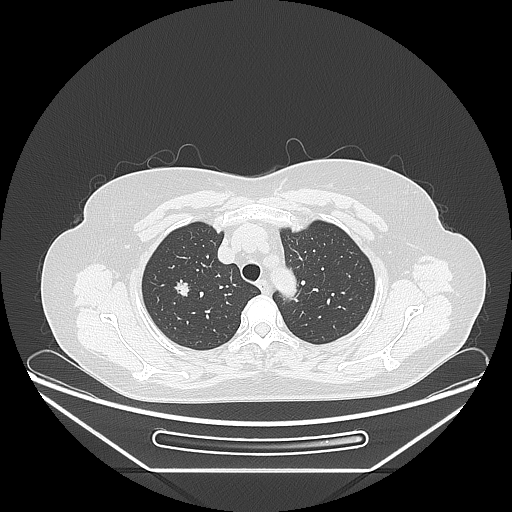
Chest CT, one axial slice; slice 197 of 236 in the series (ordered by position); 120 kVp; lung window (W 1500 / L -600 HU); 512 × 512 image matrix, field of view 433 × 433 mm. Female patient, age 60 years. Case-level facts recorded for this patient, not image findings: clinical TNM (as recorded): T1c N0 M0; histopathological grade: G2-3.
Annotated regions visible in this slice (rectangle marked by the reading radiologist):
- lung tumour (recorded histology: adenocarcinoma): box from (x=170, y=274) to (x=194, y=303) px